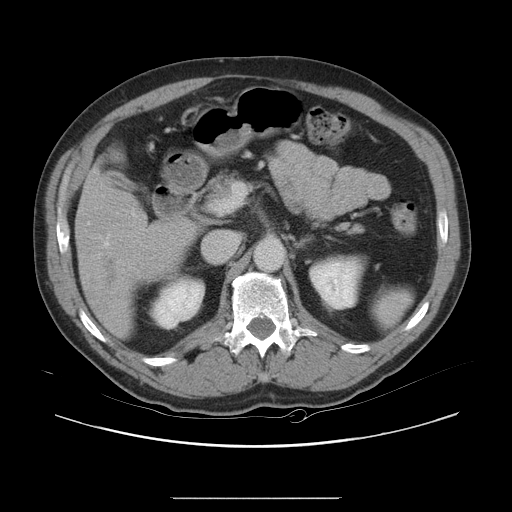
Contrast-enhanced abdominal CT, one axial slice; position 11 of 40 along the scan axis; 120 kVp; intravenous contrast given; soft-tissue window (W 400 / L 40 HU); 5 mm slice thickness; 512 × 512 image matrix, field of view 408 × 408 mm. Male patient, age 64 years. From the clinical record (not read from this slice): diagnosis: colorectal cancer liver metastases, imaged before liver resection; multiple liver metastases: yes; largest metastasis: 3.2 cm; disease in both lobes: yes.
Annotated regions visible in this slice (manually delineated by an expert):
- hepatic veins: box from (x=104, y=242) to (x=109, y=248) px
- liver: (x=76, y=177)–(x=194, y=334)
- planned liver remnant (the part of the liver to remain after resection): (x=91, y=178)–(x=102, y=185)
- liver metastasis: (x=100, y=259)–(x=120, y=288)